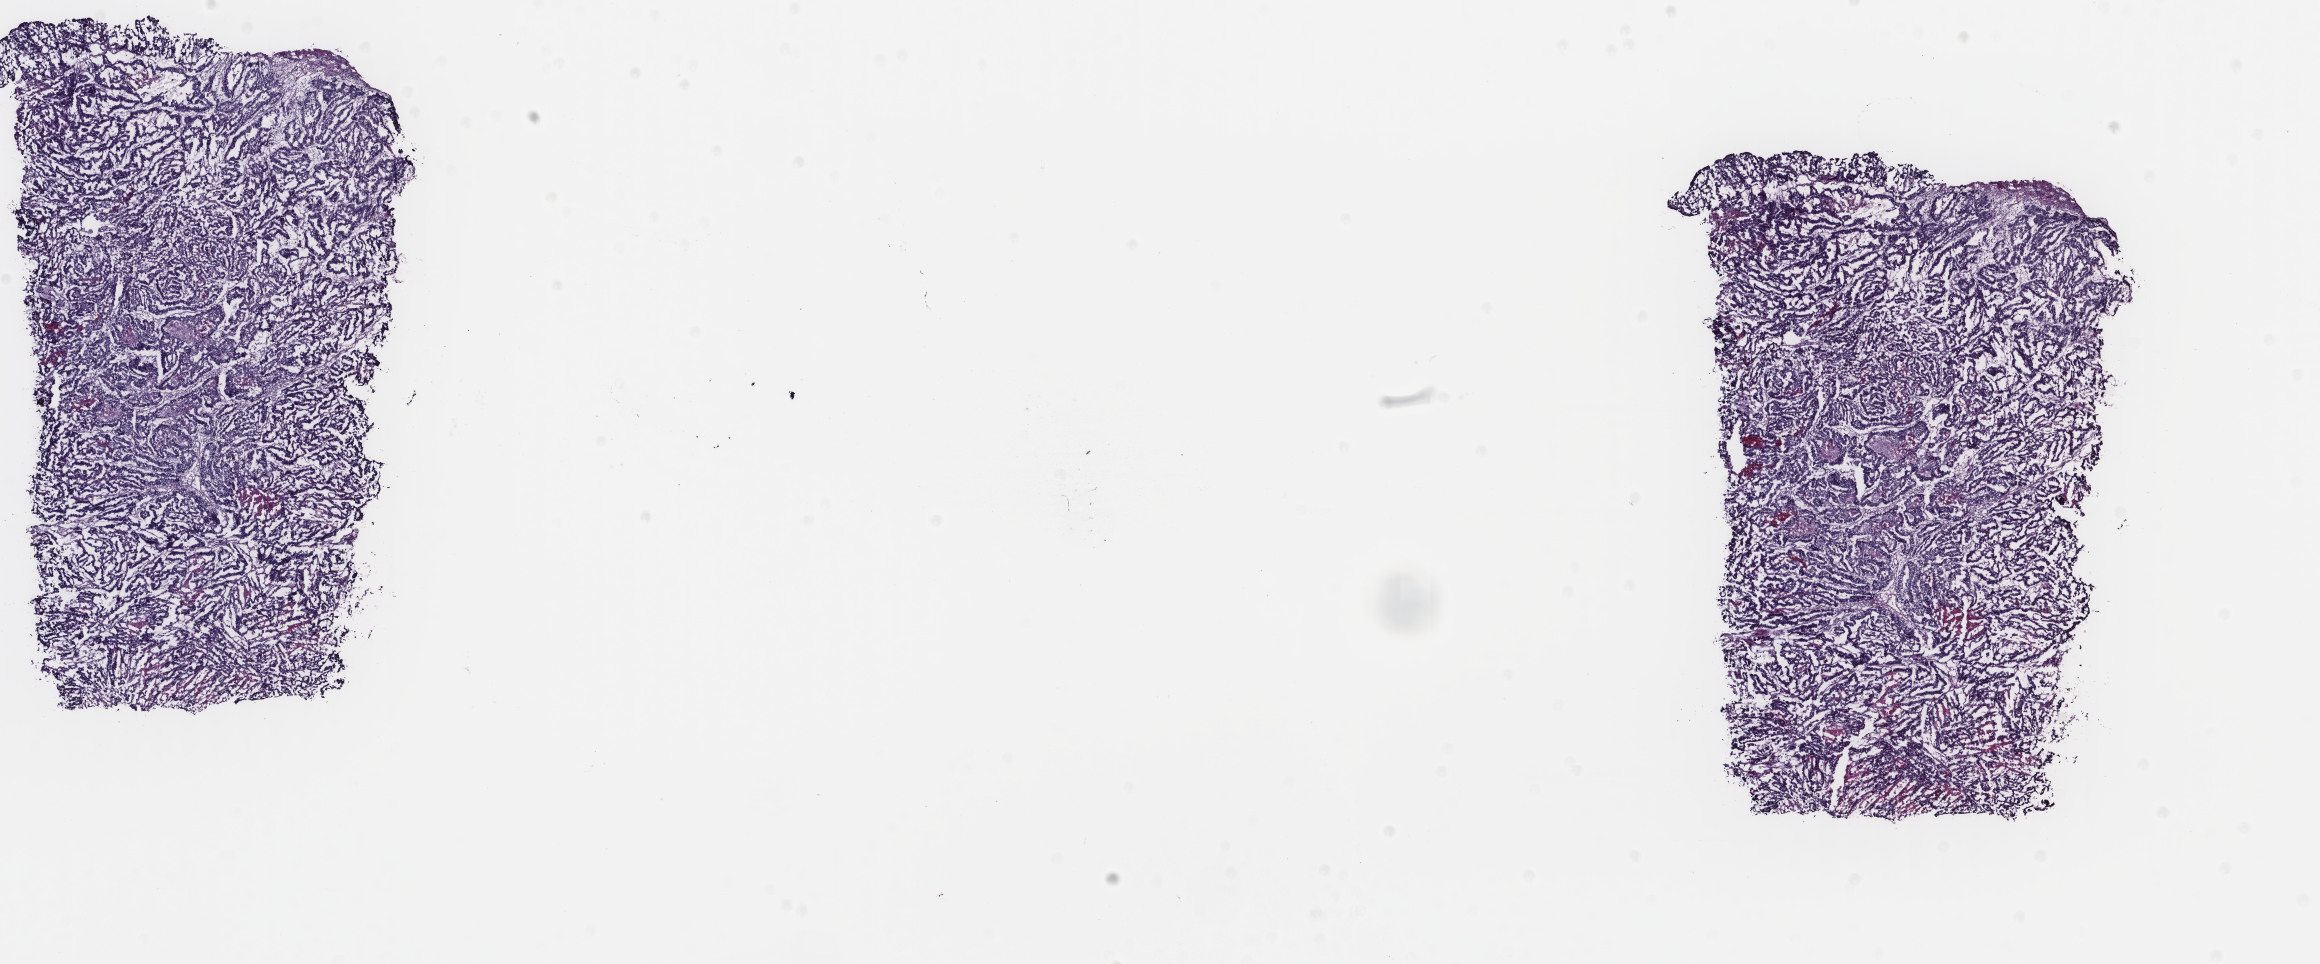
Whole-slide histology image, H&E-stained — shown as a low-resolution overview of the whole scanned area (about 18.4 x 7.7 mm, acquisition: 40x scan). Frozen section. Uterus, primary tumour sample. Female, age 65 years at initial diagnosis. Histologic grade: G2 (moderately differentiated). Composition of this section per pathologist review: tumour cells 80%, tumour nuclei 80%, normal cells 0%, stromal cells 10%, necrosis 10%. Infiltration values recorded for this section: lymphocyte infiltration 40%, monocyte infiltration 20%, neutrophil infiltration 20%.
• FIGO stage: IIIC1
• pathologic diagnosis: Endometrioid adenocarcinoma, NOS (endometrium)
• lymph nodes positive (case pathology): 1 of 17 examined